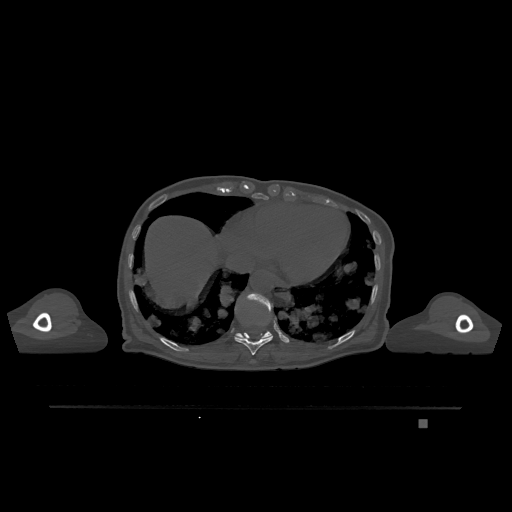
CT including the spine, one axial slice. Position 625 of 1317 along the scan axis. Bone window (W 1800 / L 400 HU). 0.5 mm slice thickness. 512 × 512 image matrix, field of view 500 × 500 mm. Patient: female, 74 years. From the clinical record (not read from this slice): primary cancer: lung.
Annotated regions visible in this slice (semi-automatically segmented with operator editing):
- T10 vertebra: bounding box <234,333,273,355> (left, top, right, bottom; pixels)
- T11 vertebra: <236,293,275,338>